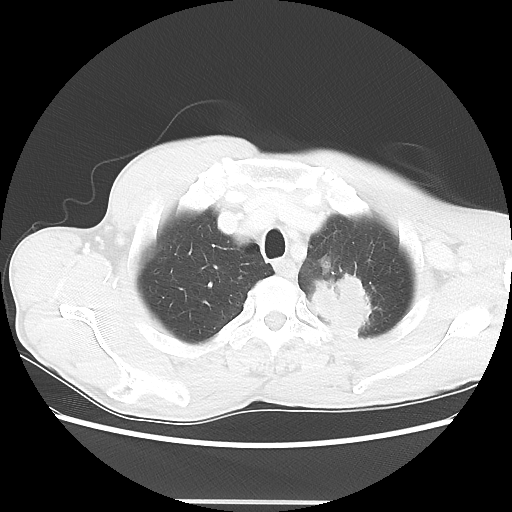
Chest CT, one axial slice; position 56 of 62 along the scan axis; reconstruction kernel LUNG; lung window (W 1500 / L -600 HU); 5 mm slice thickness; 512 × 512 image matrix, field of view 360 × 360 mm. Patient: male, 61 years. From the clinical record (not read from this slice): clinical TNM (as recorded): T3 N1 M1.
Annotated regions visible in this slice (rectangle marked by the reading radiologist):
- lung tumour (recorded histology: adenocarcinoma): bounding box [x1, y1, x2, y2] px = [310, 265, 376, 345]